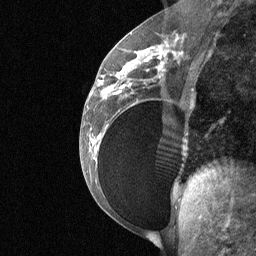
Breast MRI (dynamic contrast-enhanced), one sagittal slice. Slice 31 of 64 in the series (ordered by position). Dynamic contrast-enhanced study with each time point stored as its own series, time point 2 of 3 at this slice position (early post-contrast, ordered by acquisition time). 1.5 T. TE 4.8 ms, TR 27 ms. 2 mm slice thickness. 256 × 256 image matrix. Patient: female, 34 years. Case-level facts recorded for this patient, not image findings: setting: breast cancer imaged before/during neoadjuvant chemotherapy; receptor status: HR-positive, HER2-negative.
Annotated regions visible in this slice (semi-automatic segmentation, software-assisted and operator-edited):
- analysis volume of interest (the breast-tissue region the enhancement analysis was run in; not a lesion): box from (x=92, y=50) to (x=188, y=185) px
- tumour enhancement mask (voxels above the 90 % enhancement threshold inside the analysis volume of interest): (x=92, y=50)–(x=163, y=141)